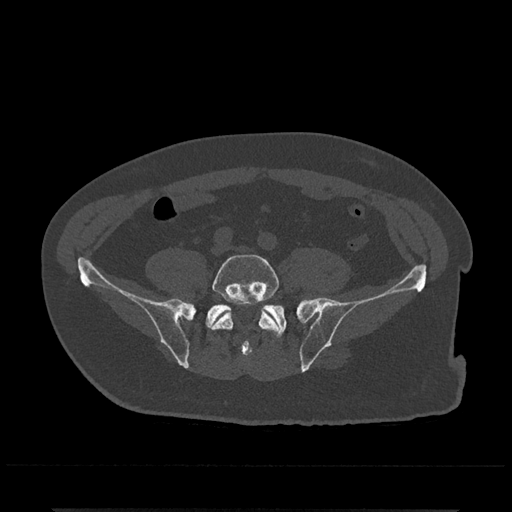
CT including the spine, one axial slice; slice 67 of 797 in the series (ordered by position); 120 kVp; bone window (W 1800 / L 400 HU); 0.5 mm slice thickness; 512 × 512 image matrix, field of view 393 × 393 mm. Patient: male, 67 years. From the clinical record (not read from this slice): primary cancer: prostate.
Outlined on this slice (semi-automatic segmentation, software-assisted and operator-edited):
- L5 vertebra: box from (x=210, y=254) to (x=279, y=352) px